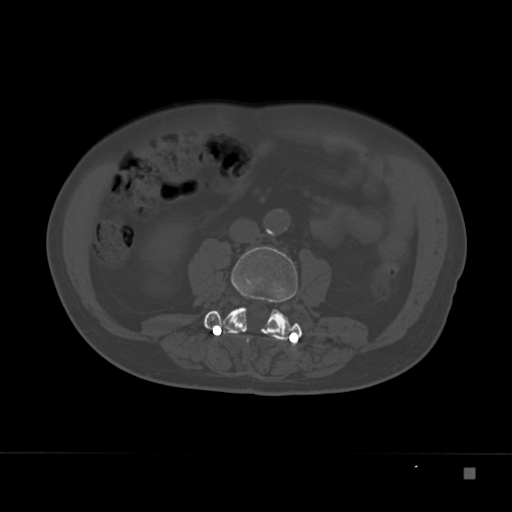
CT including the spine, one axial slice; position 61 of 332 along the scan axis; 120 kVp; bone window (W 1800 / L 400 HU); 1.5 mm slice thickness; 512 × 512 image matrix, field of view 389 × 389 mm. Male patient, age 72 years. From the clinical record (not read from this slice): primary cancer: skeletal.
Structures marked on this image (semi-automatic segmentation, software-assisted and operator-edited):
- L3 vertebra: box from (x=204, y=246) to (x=302, y=340) px
- L4 vertebra: (x=217, y=311)–(x=298, y=343)